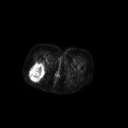
FDG PET of an extremity soft-tissue mass (from a PET/CT study), one axial slice; slice 48 of 267 in the series (ordered by position); 3.27 mm slice thickness; 128 × 128 image matrix, field of view 700 × 700 mm. Female patient, age 70 years. Case-level facts recorded for this patient, not image findings: histological type: synovial sarcoma; grade: intermediate; site of the primary tumour: right buttock.
Annotated regions visible in this slice (expert contour drawn on MRI and transferred to this co-registered scan by the dataset authors):
- gross tumour volume including surrounding oedema: bounding box (x1, y1, x2, y2) in pixels: (29, 62, 45, 81)
- gross tumour volume (mass): (29, 62, 45, 81)